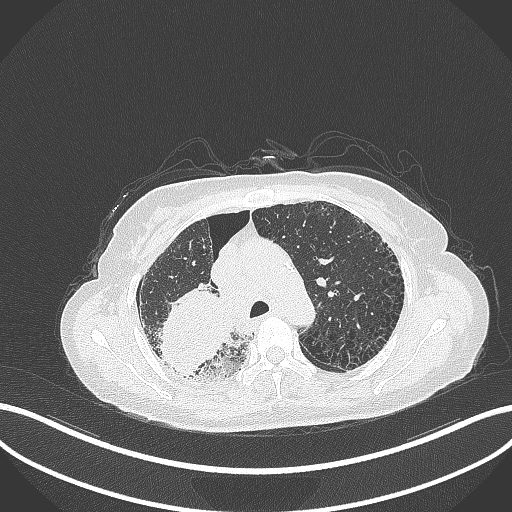
Chest CT, one axial slice; position 247 of 408 along the scan axis; reconstruction kernel B70f; 120 kVp; lung window (W 1500 / L -600 HU); 1 mm slice thickness; 512 × 512 image matrix. Female patient, age 64 years. From the clinical record (not read from this slice): clinical TNM (as recorded): T3 N3 M0.
Outlined on this slice (rectangle marked by the reading radiologist):
- lung tumour (recorded histology: squamous cell carcinoma): bounding box [x1, y1, x2, y2] px = [153, 284, 234, 375]